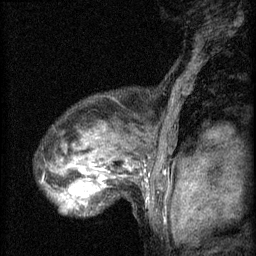
Breast MRI (dynamic contrast-enhanced), one sagittal slice; slice 48 of 60 in the series (ordered by position); 3 images stored at this slice position (order not interpretable as contrast timing); 1.5 T; TE 4.2 ms, TR 8.2 ms; 2 mm slice thickness; 256 × 256 image matrix. Patient: female, 48 years.
Structures marked on this image (semi-automatic segmentation, software-assisted and operator-edited):
- analysis volume of interest (the breast-tissue region the enhancement analysis was run in; not a lesion): box from (x=52, y=160) to (x=125, y=215) px
- tumour enhancement mask (voxels above the 70 % enhancement threshold inside the analysis volume of interest): (x=68, y=168)–(x=106, y=207)